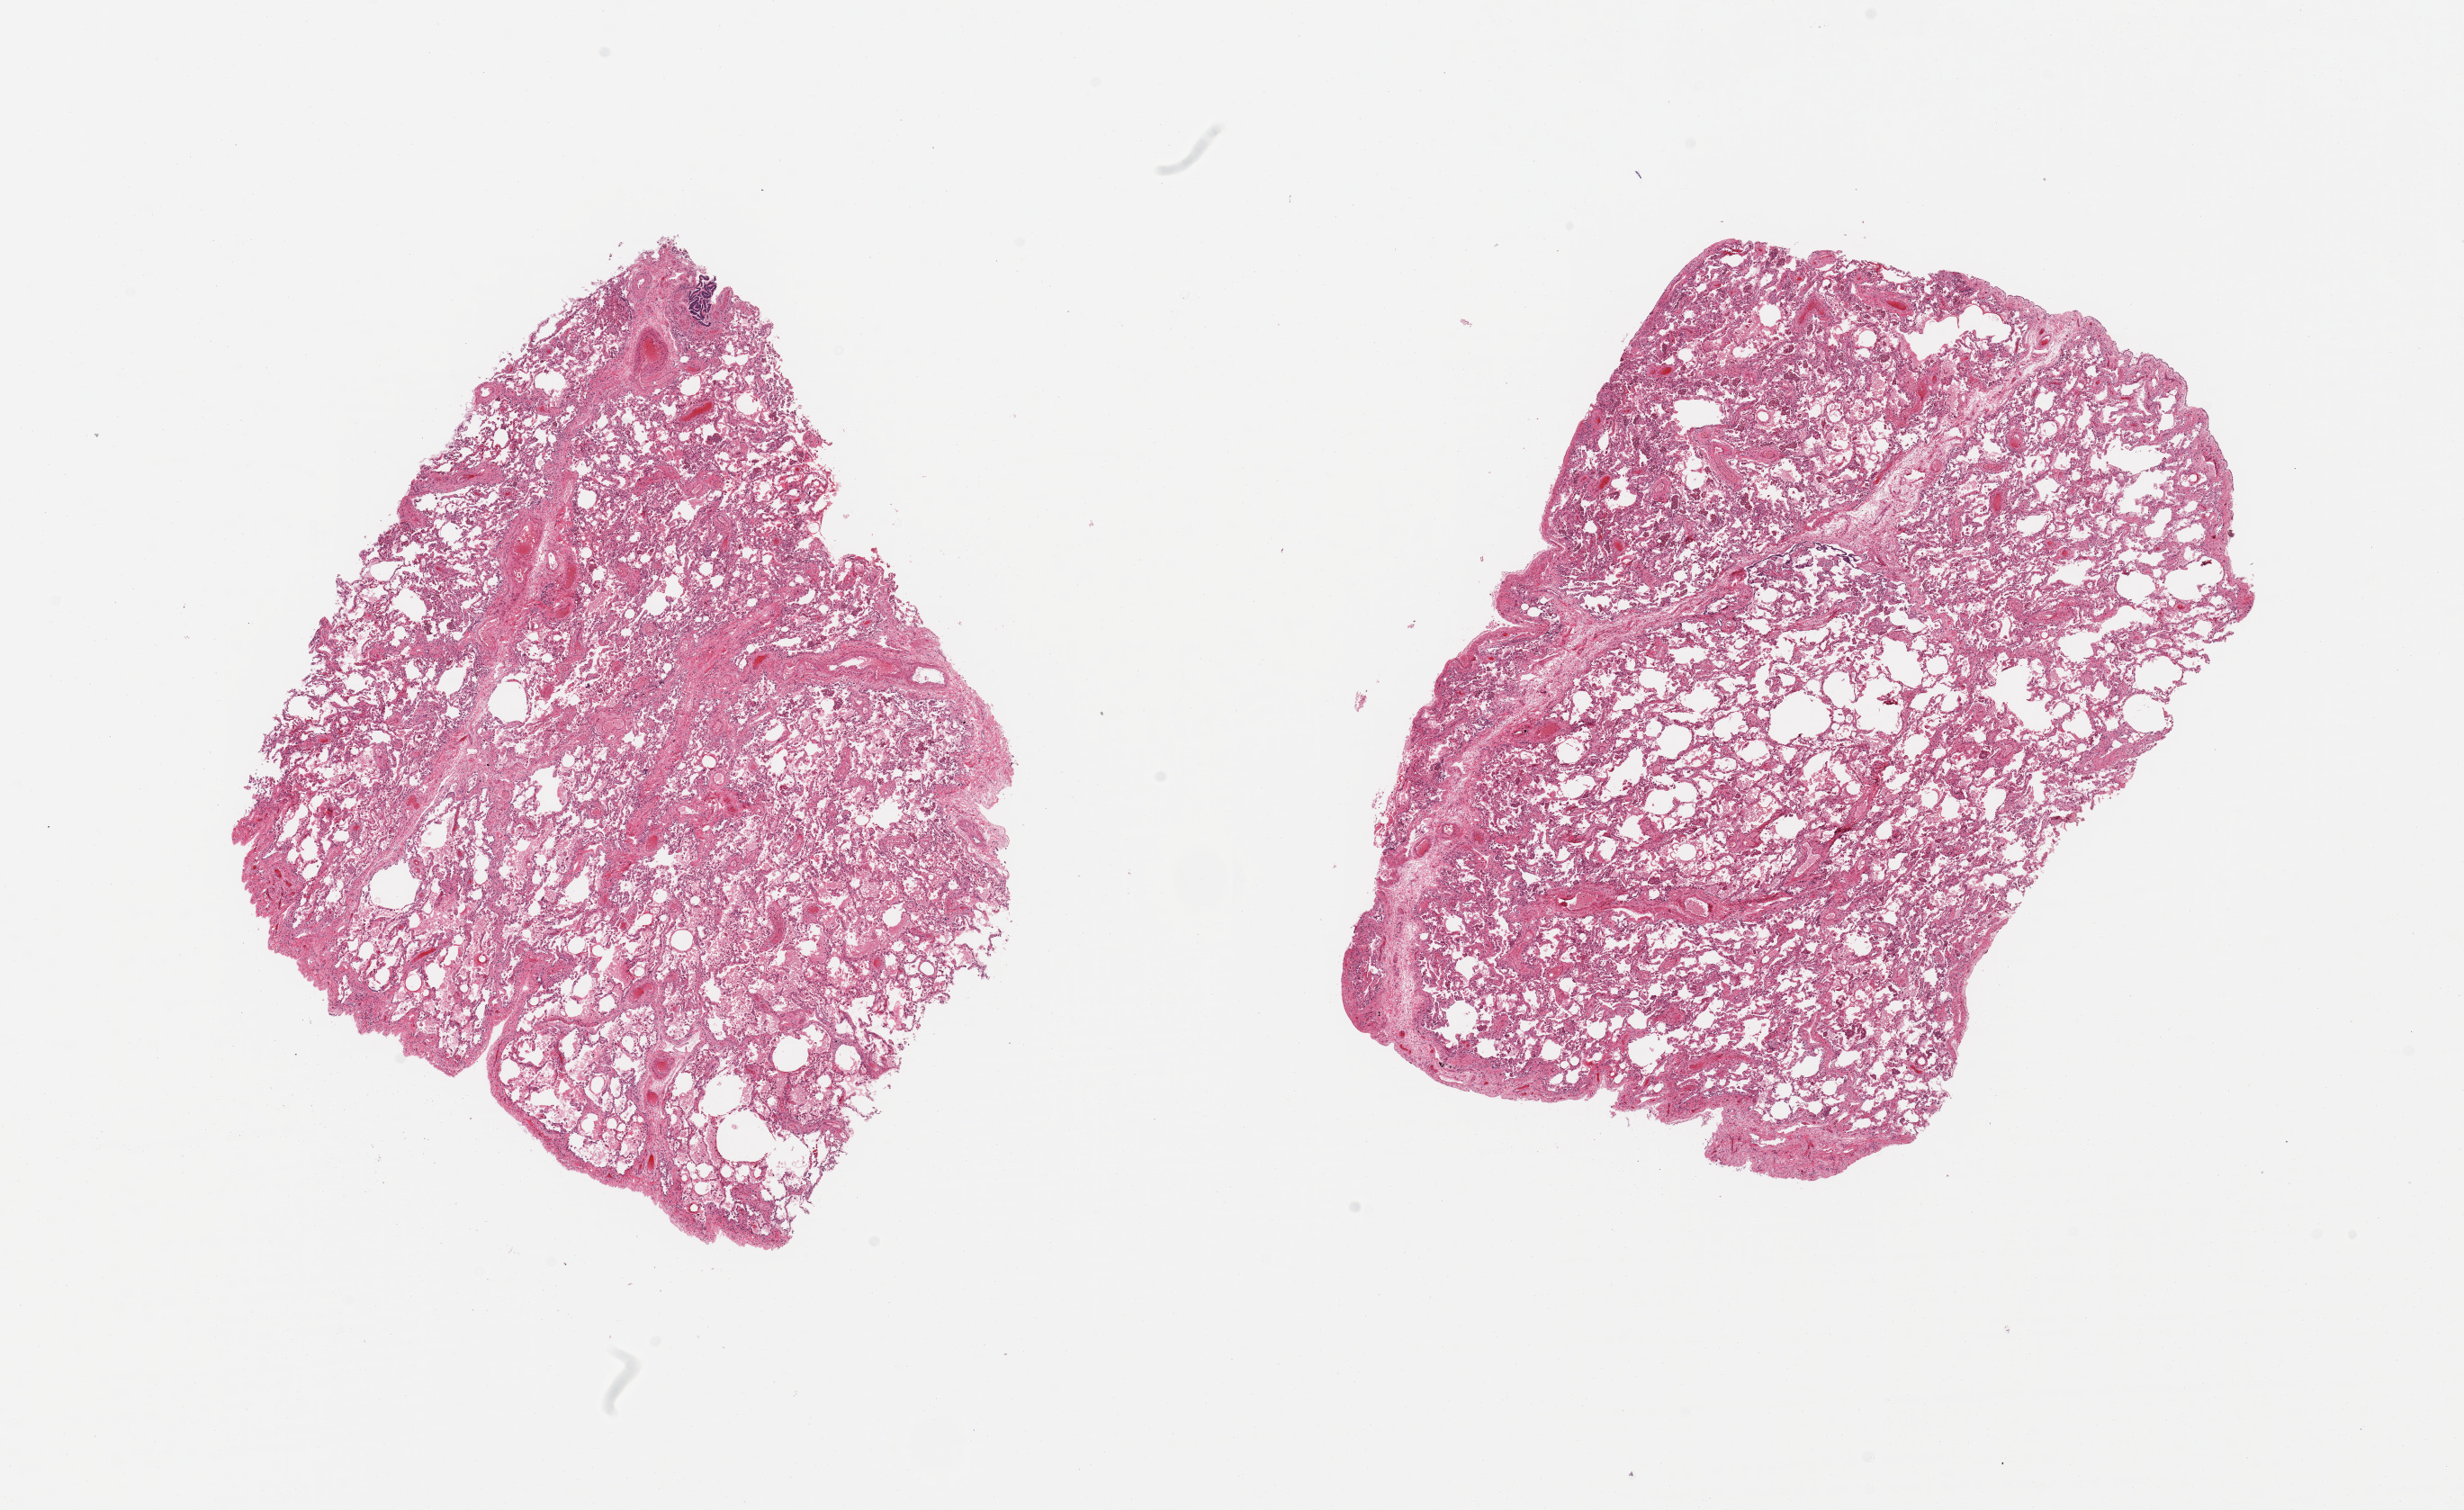
Hematoxylin and eosin (H&E) whole-slide image — a low-resolution overview of the entire scanned area, about 21.7 x 13.3 mm (slide scanned at 20x), PAXgene-fixed, paraffin-embedded tissue, target tissue: lung, donor tissue sample. Donor: male.
- pathologist's review note for this sample: 2 pieces; includes pleura (target is 1cm below pleura), congestion, many macrophages